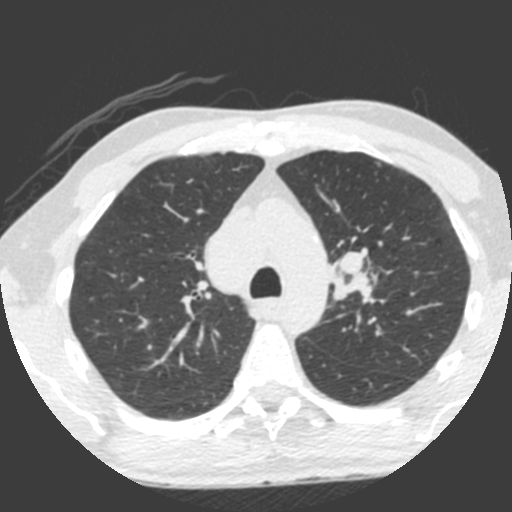
Low-dose screening chest CT, one axial slice. Slice 155 of 212 in the series (ordered by position). Lung window (W 1500 / L -600 HU). 2 mm slice thickness. 512 × 512 image matrix.
Outlined on this slice (expert manual segmentation):
- lesion 1 (tumor, upper lobe of left lung): bounding box [x1, y1, x2, y2] px = [329, 246, 375, 305]